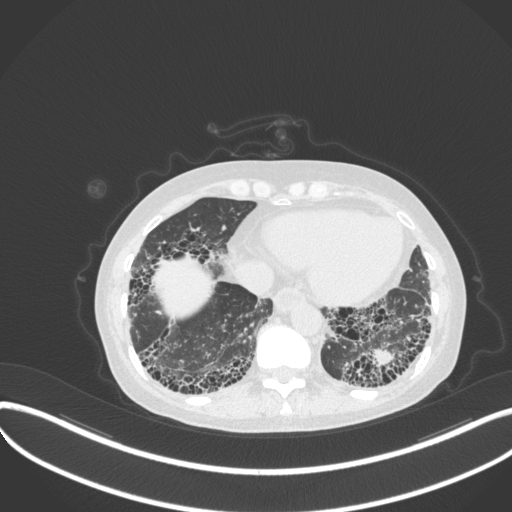
Chest CT, one axial slice; reconstruction kernel B31f; 120 kVp; lung window (W 1500 / L -600 HU); 1 mm slice thickness; 512 × 512 image matrix, field of view 400 × 400 mm. Patient: female, 56 years. From the clinical record (not read from this slice): clinical TNM (as recorded): T1 N0 M0.
Annotated regions visible in this slice (bounding box drawn by a radiologist):
- lung tumour (recorded histology: adenocarcinoma): box from (x=367, y=346) to (x=398, y=371) px